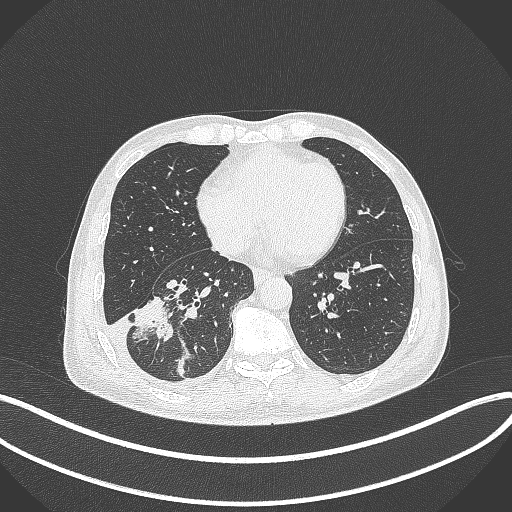
Chest CT, one axial slice; slice 140 of 388 in the series (ordered by position); reconstruction kernel B70f; lung window (W 1500 / L -600 HU); 512 × 512 image matrix, field of view 400 × 400 mm. Patient: male, 64 years. Case-level facts recorded for this patient, not image findings: clinical TNM (as recorded): T3 N0 M0; histopathological grade: G2-3.
Annotated regions visible in this slice (rectangle marked by the reading radiologist):
- lung tumour (recorded histology: adenocarcinoma): bounding box <130,286,177,349> (left, top, right, bottom; pixels)